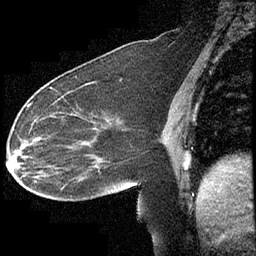
Breast MRI (dynamic contrast-enhanced), one sagittal slice; position 160 of 232 along the scan axis; dynamic contrast-enhanced study with each time point stored as its own series, time point 2 of 4 at this slice position (early post-contrast, ordered by acquisition time); 1.5 T; TE 4.2 ms, TR 6.7 ms; 3 mm slice thickness; 256 × 256 image matrix, field of view 200 × 200 mm. Female patient, age 63 years. Case-level facts recorded for this patient, not image findings: setting: breast cancer imaged before/during neoadjuvant chemotherapy; receptor status: triple-negative.
Outlined on this slice (semi-automatic segmentation, software-assisted and operator-edited):
- analysis volume of interest (the breast-tissue region the enhancement analysis was run in; not a lesion): bounding box (x1, y1, x2, y2) in pixels: (13, 90, 140, 211)
- tumour enhancement mask (voxels above the 70 % enhancement threshold inside the analysis volume of interest): (28, 91, 73, 125)